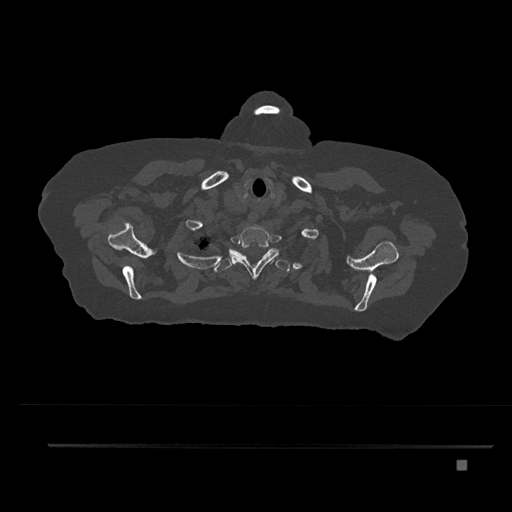
CT including the spine, one axial slice. Position 689 of 797 along the scan axis. Reconstruction kernel Br40s/3. 120 kVp. Bone window (W 1800 / L 400 HU). 512 × 512 image matrix. Patient: female, 76 years. Case-level facts recorded for this patient, not image findings: primary cancer: lung; vertebrae with lytic lesions (as recorded): T11, L3.
Outlined on this slice (semi-automatic segmentation, software-assisted and operator-edited):
- T1 vertebra: bounding box [x1, y1, x2, y2] px = [229, 225, 279, 280]
- T2 vertebra: [207, 248, 290, 272]